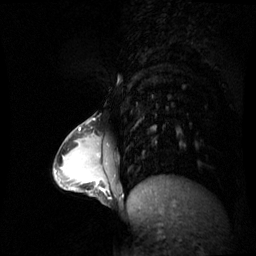
Breast MRI (dynamic contrast-enhanced), one sagittal slice. Position 19 of 60 along the scan axis. Dynamic contrast-enhanced series, image 2 of 3 at this slice position (ordered by acquisition). 1.5 T. TE 4.2 ms, TR 8.9 ms. 256 × 256 image matrix, field of view 300 × 300 mm. Patient: female, 34 years. Case-level facts recorded for this patient, not image findings: setting: breast cancer imaged before/during neoadjuvant chemotherapy; receptor status: triple-negative.
Annotated regions visible in this slice (semi-automatically segmented with operator editing):
- analysis volume of interest (the breast-tissue region the enhancement analysis was run in; not a lesion): box from (x=65, y=168) to (x=108, y=193) px
- tumour enhancement mask (voxels above the 70 % enhancement threshold inside the analysis volume of interest): (x=96, y=180)–(x=104, y=191)